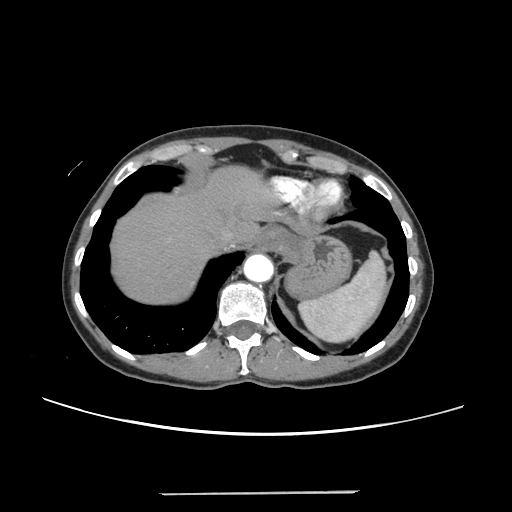
Contrast-enhanced abdominal CT, one axial slice. Position 210 of 240 along the scan axis. Intravenous contrast given. Soft-tissue window (W 400 / L 40 HU). 1.25 mm slice thickness. 512 × 512 image matrix. Female patient, age 60 years. From the clinical record (not read from this slice): diagnosis: colorectal cancer liver metastases, imaged before liver resection; multiple liver metastases: no; largest metastasis: 1.5 cm.
Structures marked on this image (expert manual segmentation):
- hepatic veins: bounding box (x1, y1, x2, y2) in pixels: (221, 230, 233, 241)
- liver: (112, 168, 270, 304)
- planned liver remnant (the part of the liver to remain after resection): (112, 168, 270, 304)